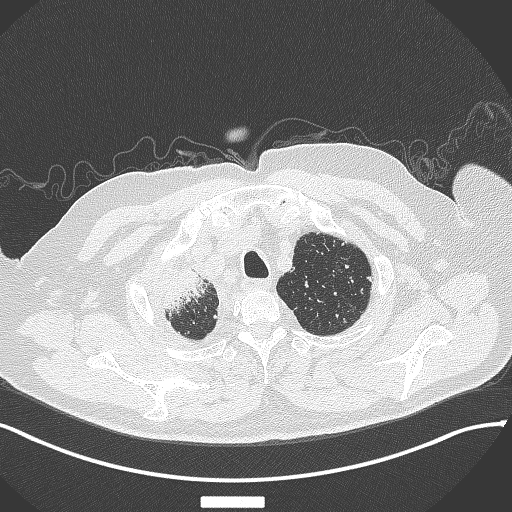
Chest CT, one axial slice; slice 326 of 384 in the series (ordered by position); 120 kVp; lung window (W 1500 / L -600 HU); 1 mm slice thickness; 512 × 512 image matrix, field of view 400 × 400 mm. Patient: male, 69 years. Case-level facts recorded for this patient, not image findings: clinical TNM (as recorded): T4 N3 M1.
Outlined on this slice (rectangle marked by the reading radiologist):
- lung tumour (recorded histology: adenocarcinoma): box from (x=161, y=261) to (x=224, y=316) px